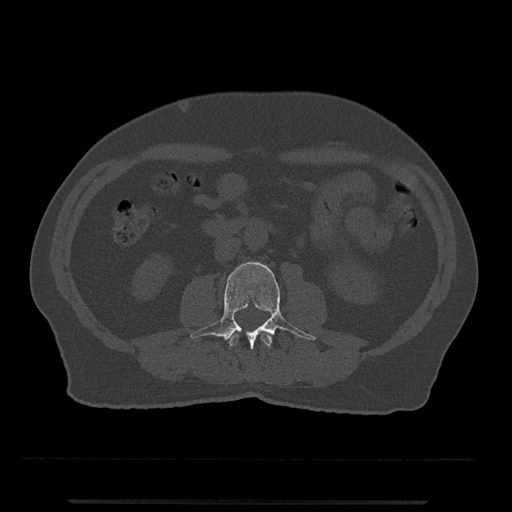
CT including the spine, one axial slice; position 208 of 797 along the scan axis; reconstruction kernel Br40s/3; 120 kVp; bone window (W 1800 / L 400 HU); 0.5 mm slice thickness; 512 × 512 image matrix. Male patient, age 63 years. Case-level facts recorded for this patient, not image findings: primary cancer: prostate.
Structures marked on this image (semi-automatic segmentation, software-assisted and operator-edited):
- L2 vertebra: bounding box <229,333,272,348> (left, top, right, bottom; pixels)
- L3 vertebra: <190,262,316,350>